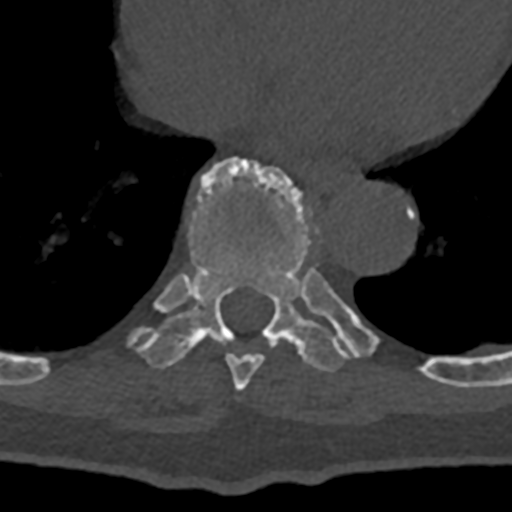
CT including the spine, one axial slice; slice 675 of 797 in the series (ordered by position); reconstruction kernel Br40s/3; 120 kVp; bone window (W 1800 / L 400 HU); 0.5 mm slice thickness; 512 × 512 image matrix, field of view 160 × 160 mm. Patient: male, 74 years. Case-level facts recorded for this patient, not image findings: primary cancer: renal; vertebrae with lytic lesions (as recorded): T10, L1, L2, L3, L4, L5.
Structures marked on this image (semi-automatic segmentation, software-assisted and operator-edited):
- T8 vertebra: bounding box <225,353,264,390> (left, top, right, bottom; pixels)
- T9 vertebra: <128,158,432,378>